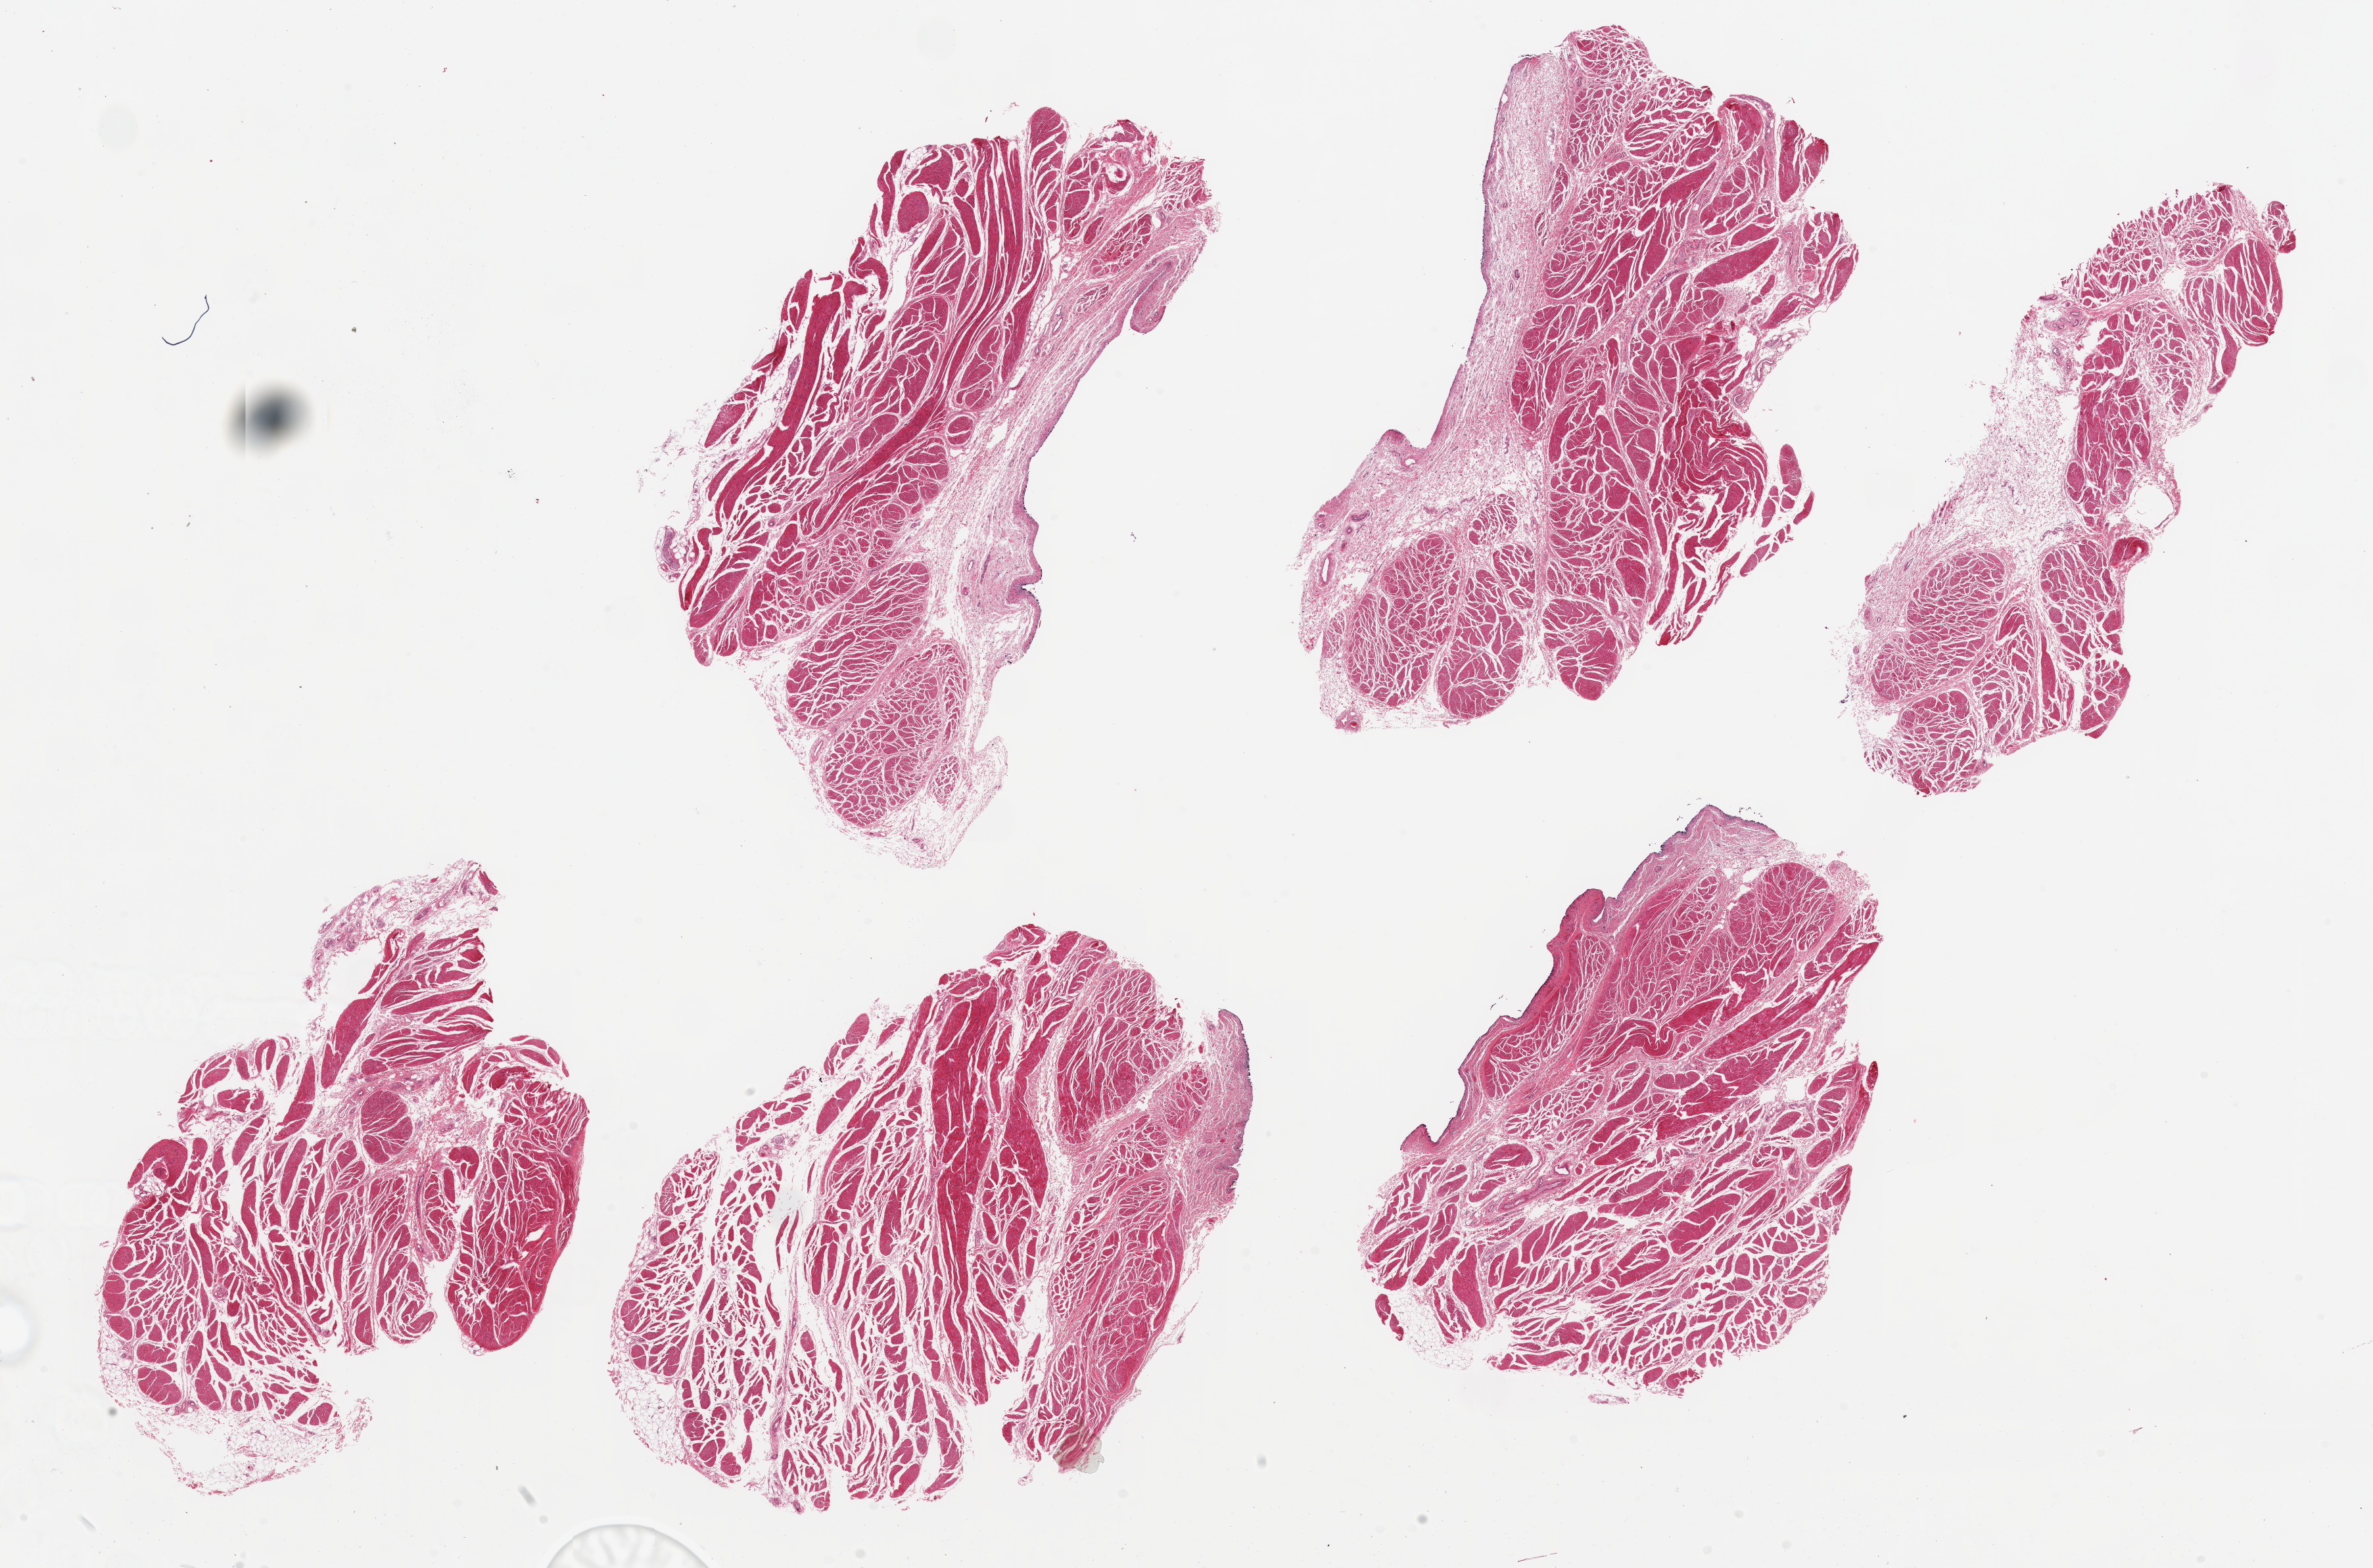
Whole-slide image, haematoxylin and eosin stain, brightfield — shown as a low-resolution overview of the whole scanned area (about 28.5 x 18.9 mm, acquisition: 20x scan), PAXgene-fixed paraffin-embedded (PFPE) section, sampled site (target tissue): urinary bladder, donor tissue sample.
- reviewer comment on this tissue sample: 6 pieces up to 9x5 mm; mucosa sloughed; muscle in good shape